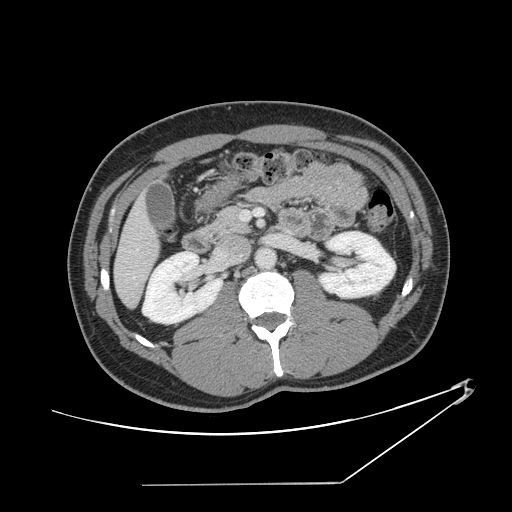
Contrast-enhanced abdominal CT, one axial slice. Position 56 of 152 along the scan axis. Reconstruction kernel STANDARD. Intravenous contrast given. Soft-tissue window (W 400 / L 40 HU). 2.5 mm slice thickness. 512 × 512 image matrix, field of view 432 × 432 mm. Male patient, age 45 years. Case-level facts recorded for this patient, not image findings: diagnosis: colorectal cancer liver metastases, imaged before liver resection; multiple liver metastases: no; largest metastasis: 1 cm; disease in both lobes: no.
Outlined on this slice (expert manual segmentation):
- hepatic veins: box from (x=129, y=248) to (x=139, y=253) px
- liver: (x=116, y=201)–(x=158, y=306)
- planned liver remnant (the part of the liver to remain after resection): (x=116, y=201)–(x=158, y=307)
- portal vein (with intrahepatic branches): (x=240, y=209)–(x=264, y=220)